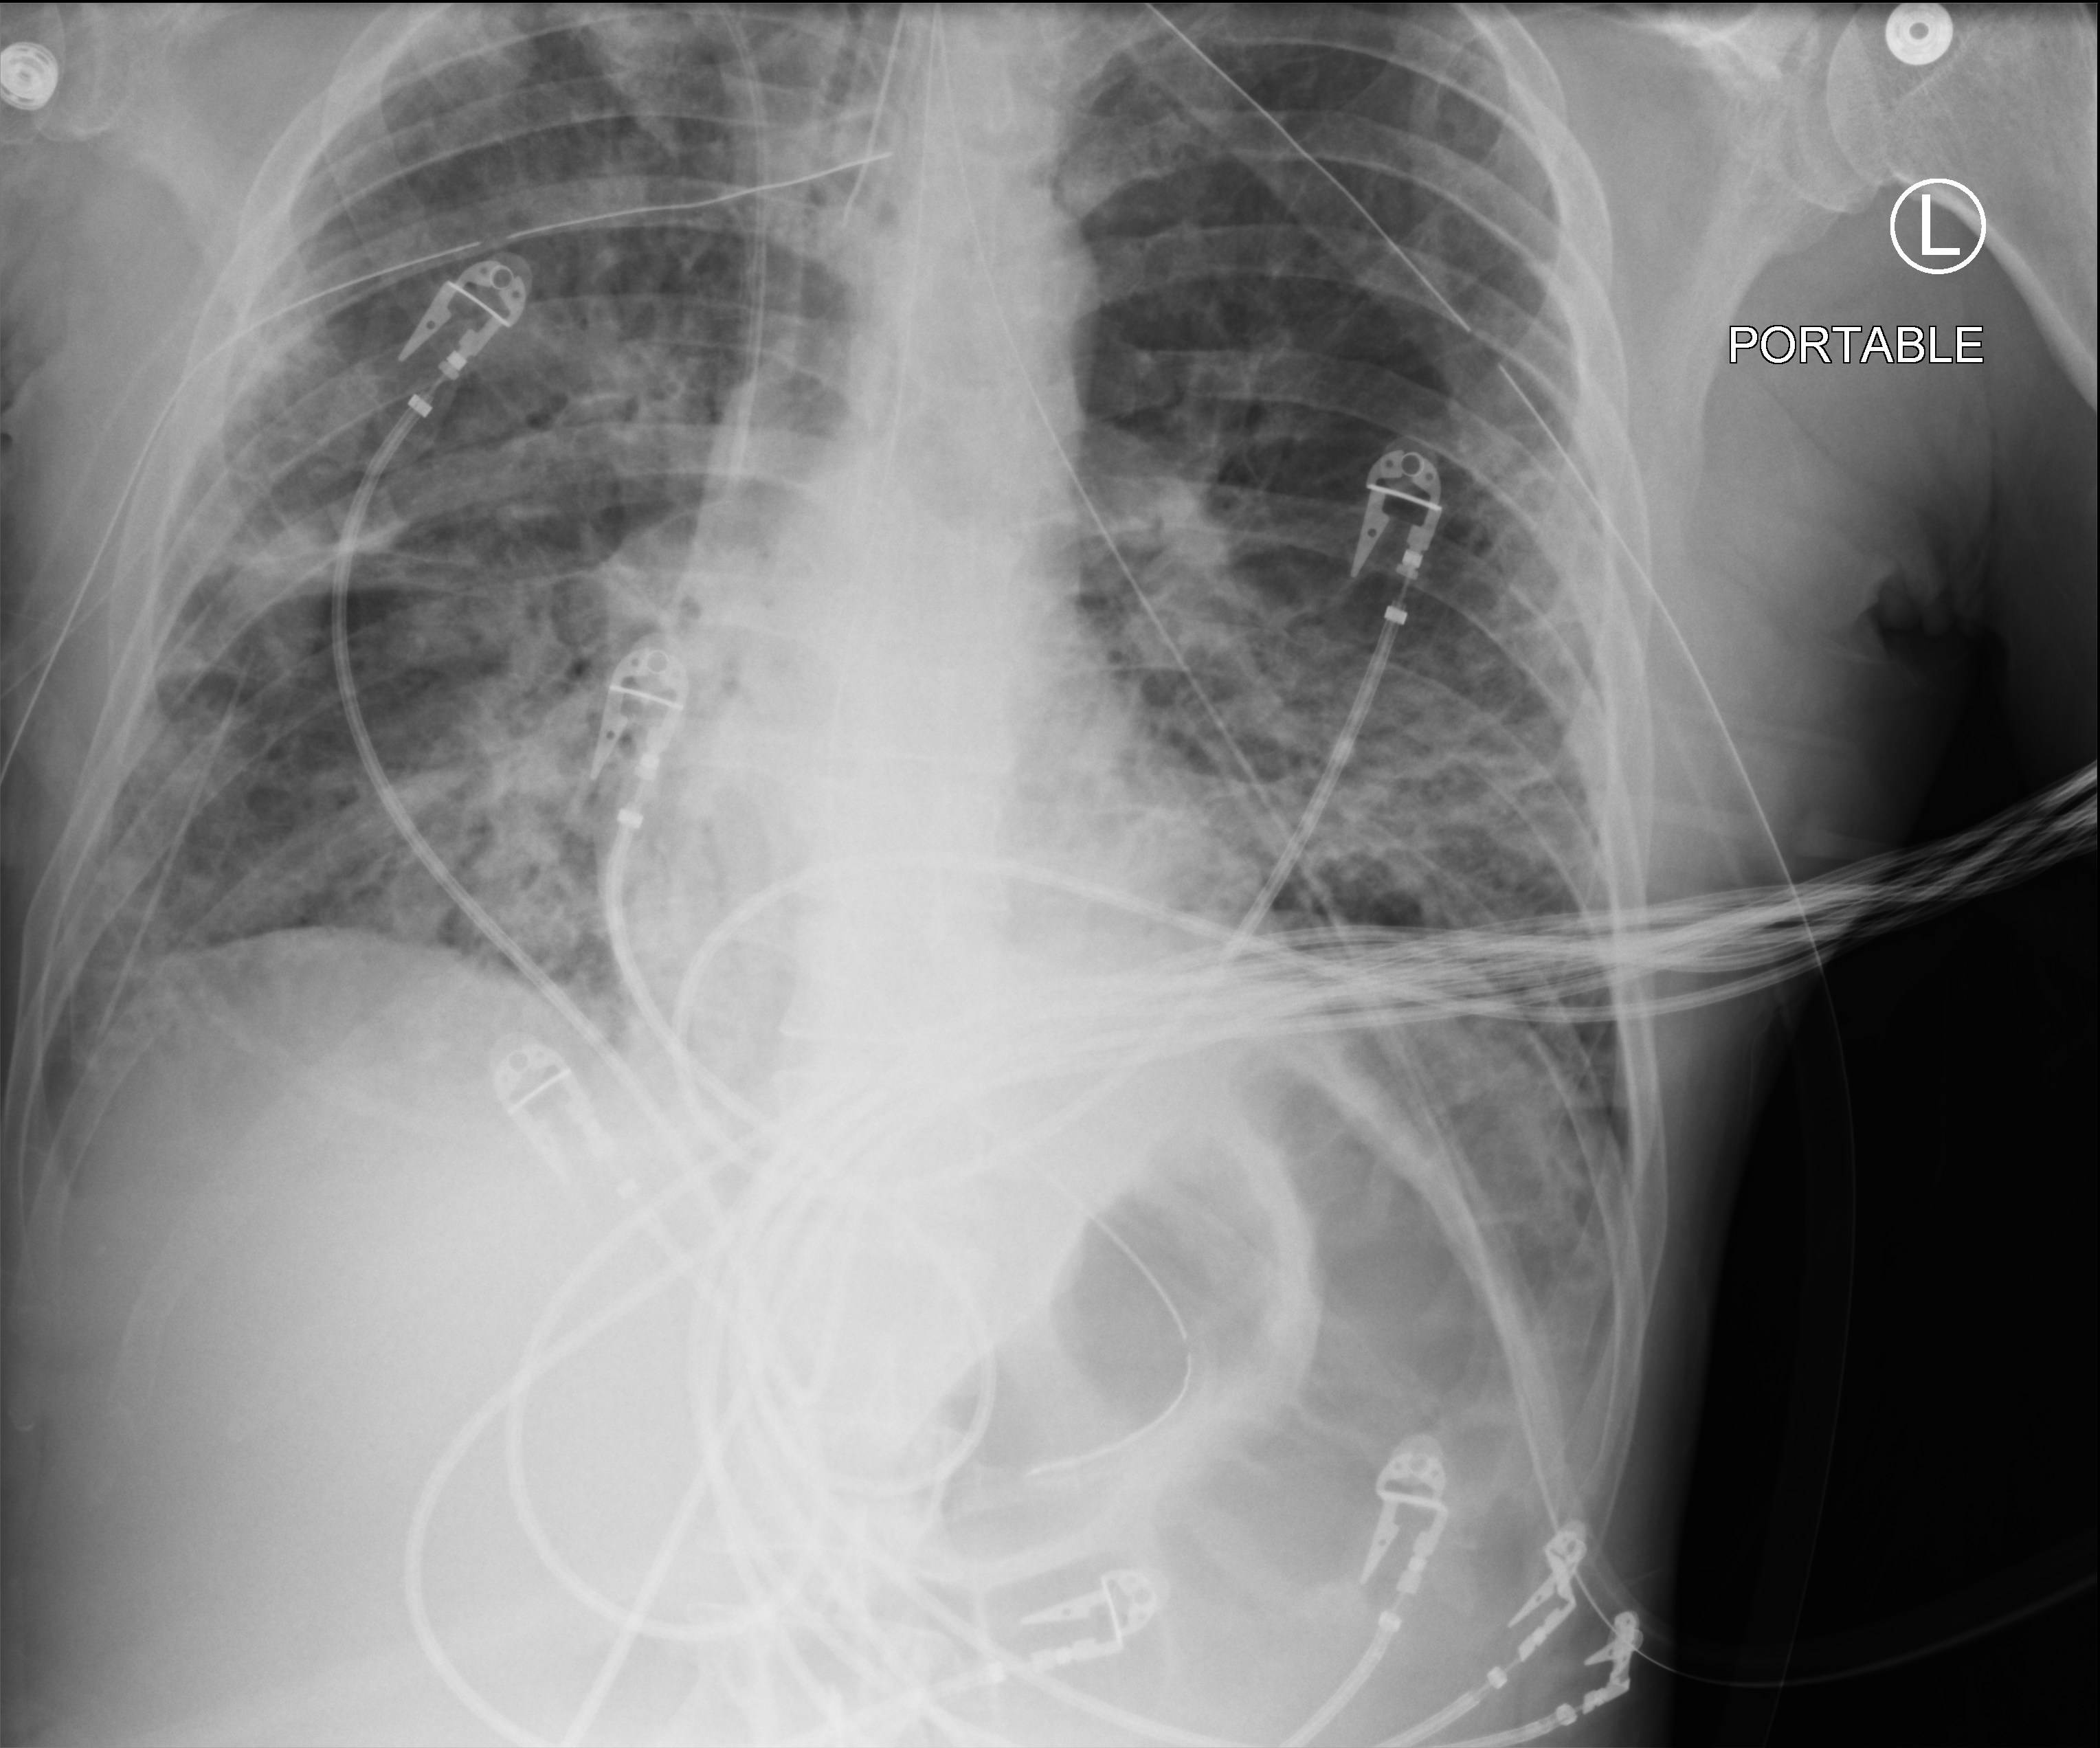
Bedside chest radiograph (computed radiography). Patient hospitalised with COVID-19; male, aged 18–59 years.
Hospital-stay facts (about this admission, not read from this image; timing relative to this image not recorded): admitted to intensive care during this hospital stay: yes; COPD (admission record): no; mechanically ventilated during this hospital stay: yes.